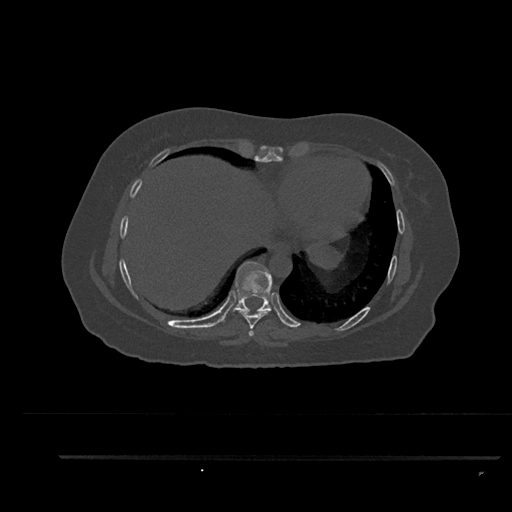
CT including the spine, one axial slice; position 438 of 797 along the scan axis; reconstruction kernel Br40s/3; 120 kVp; bone window (W 1800 / L 400 HU); 0.5 mm slice thickness; 512 × 512 image matrix, field of view 408 × 408 mm. Patient: female, 44 years. From the clinical record (not read from this slice): primary cancer: renal.
Outlined on this slice (semi-automatically segmented with operator editing):
- T7 vertebra: bounding box [x1, y1, x2, y2] px = [249, 330, 254, 336]
- T8 vertebra: [236, 309, 270, 329]
- T9 vertebra: [233, 261, 273, 312]